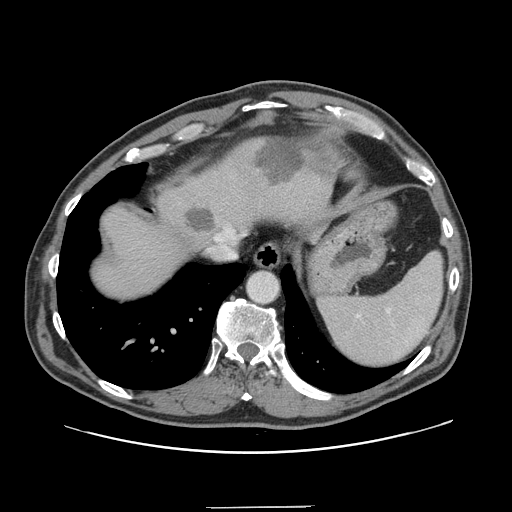
Contrast-enhanced abdominal CT, one axial slice. Intravenous contrast given. Soft-tissue window (W 400 / L 40 HU). 2.5 mm slice thickness. 512 × 512 image matrix. Male patient, age 64 years. Case-level facts recorded for this patient, not image findings: diagnosis: colorectal cancer liver metastases, imaged before liver resection; multiple liver metastases: yes; largest metastasis: 3.5 cm; disease in both lobes: yes.
Outlined on this slice (manually delineated by an expert):
- hepatic veins: bounding box [x1, y1, x2, y2] px = [225, 229, 228, 232]
- liver: [91, 135, 327, 298]
- planned liver remnant (the part of the liver to remain after resection): [91, 143, 255, 299]
- liver metastasis: [186, 210, 215, 234]
- liver metastasis: [255, 142, 305, 187]